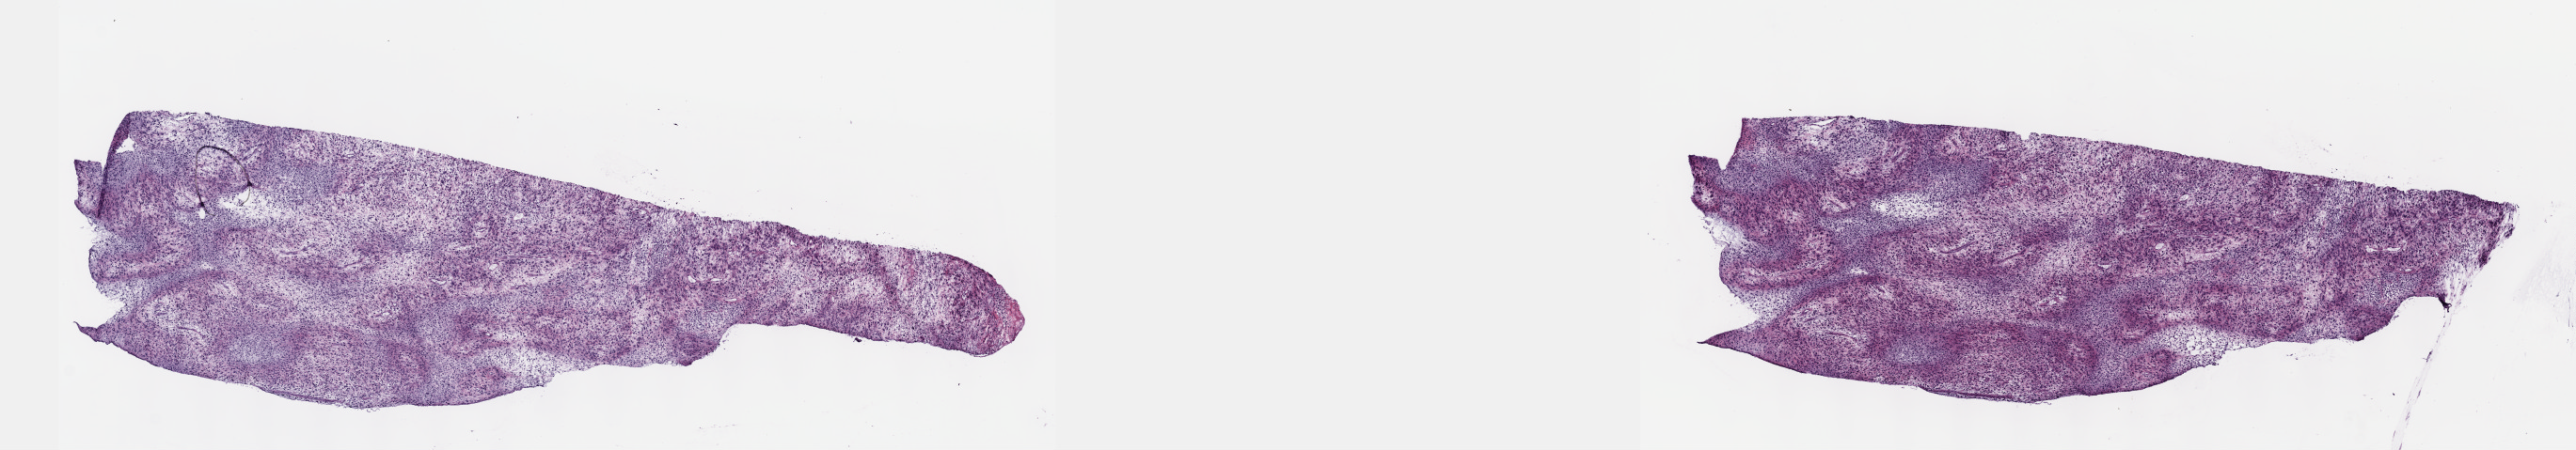
Digitized H&E tissue section (whole slide) — a low-resolution overview of the entire scanned area, about 22.1 x 3.9 mm (acquisition: 40x scan), frozen section from the top of the tissue portion, primary tumour sample from the retroperitoneum and peritoneum. Male, age 52 years at initial diagnosis. Composition of this section per pathologist review: tumour cells 80%, tumour nuclei 80%, normal cells 0%, stromal cells 20%, necrosis 0%. Infiltration values recorded for this section: lymphocyte infiltration 2%, monocyte infiltration 1%, neutrophil infiltration 2%.
Diagnosis: Undifferentiated sarcoma (retroperitoneum).